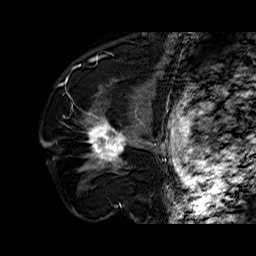
Breast MRI (dynamic contrast-enhanced), one sagittal slice; slice 42 of 60 in the series (ordered by position); dynamic contrast-enhanced series, time point 2 of 6 at this slice position (early post-contrast); 1.5 T; TE 6.4 ms, TR 32.7 ms; 4 mm slice thickness; 256 × 256 image matrix, field of view 200 × 200 mm. Female patient. From the clinical record (not read from this slice): setting: breast cancer imaged before/during neoadjuvant chemotherapy; receptor status: HR-positive, HER2-negative.
Outlined on this slice (semi-automatically segmented with operator editing):
- analysis volume of interest (the breast-tissue region the enhancement analysis was run in; not a lesion): bounding box <78,110,141,174> (left, top, right, bottom; pixels)
- tumour enhancement mask (voxels above the 100 % enhancement threshold inside the analysis volume of interest): <87,112,128,167>